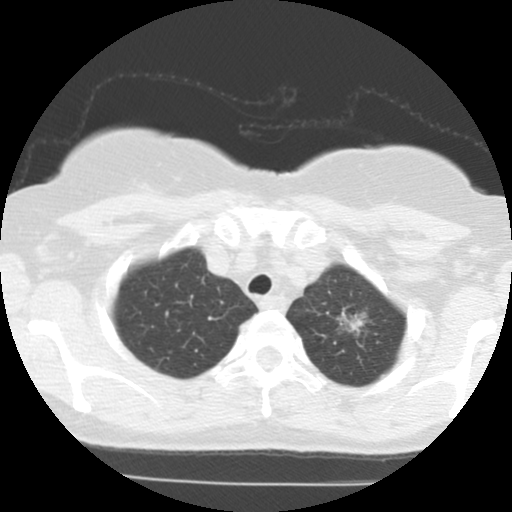
Chest CT (low-dose screening protocol), one axial image; baseline screening round; lung window (W 1500 / L -600 HU); 2.5 mm slice thickness; slice 102 of 123 in the series; 512 × 512 image matrix, field of view 290 × 290 mm. Female participant, aged 61 years at enrolment.
- Expert-annotated lung lesion, bounding box (x1, y1, x2, y2) in pixels: (323, 302, 380, 352).
- The screening reader recorded 2 non-calcified nodules or masses ≥4 mm on this exam (right lower lobe, left upper lobe); which of them this box marks is not recorded.
- Lung cancer was diagnosed 79 days after this screen: adenocarcinoma, NOS, left upper lobe, stage IIIB (AJCC 6th edition), 15 mm at pathology.